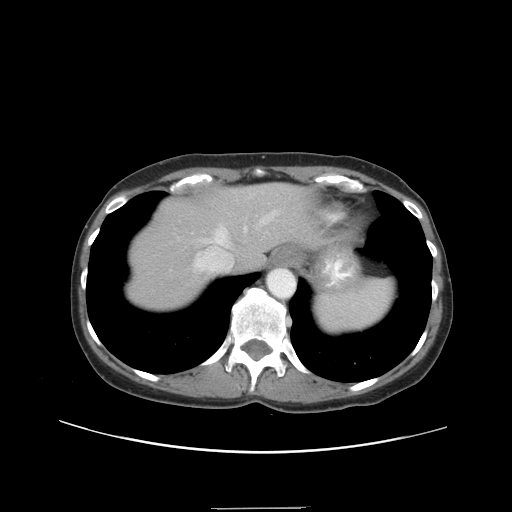
Contrast-enhanced abdominal CT, one axial slice. Position 32 of 38 along the scan axis. Reconstruction kernel STANDARD. 120 kVp. Soft-tissue window (W 400 / L 40 HU). 512 × 512 image matrix, field of view 388 × 388 mm. Female patient, age 64 years. Case-level facts recorded for this patient, not image findings: diagnosis: colorectal cancer liver metastases, imaged before liver resection; multiple liver metastases: no; largest metastasis: 3.8 cm; disease in both lobes: yes.
Annotated regions visible in this slice (expert manual segmentation):
- hepatic veins: box from (x=195, y=210) to (x=278, y=271) px
- liver: (x=129, y=186)–(x=309, y=309)
- planned liver remnant (the part of the liver to remain after resection): (x=162, y=187)–(x=309, y=270)